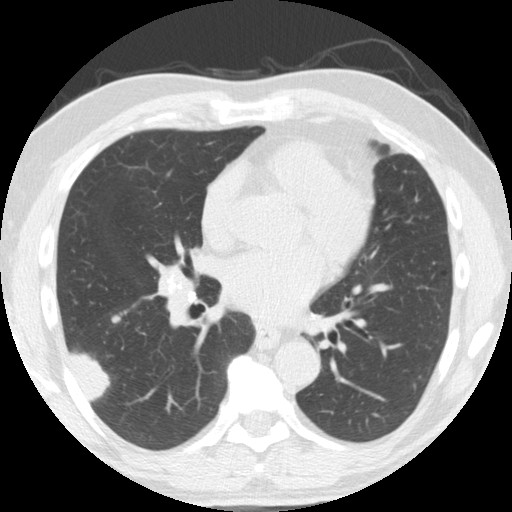
Low-dose screening chest CT, one axial slice; position 82 of 174 along the scan axis; 120 kVp; lung window (W 1500 / L -600 HU); 512 × 512 image matrix, field of view 341 × 341 mm.
Structures marked on this image (outlined manually by an expert reader):
- lesion 1 (tumor, lower lobe of right lung): bounding box [x1, y1, x2, y2] px = [71, 352, 110, 401]